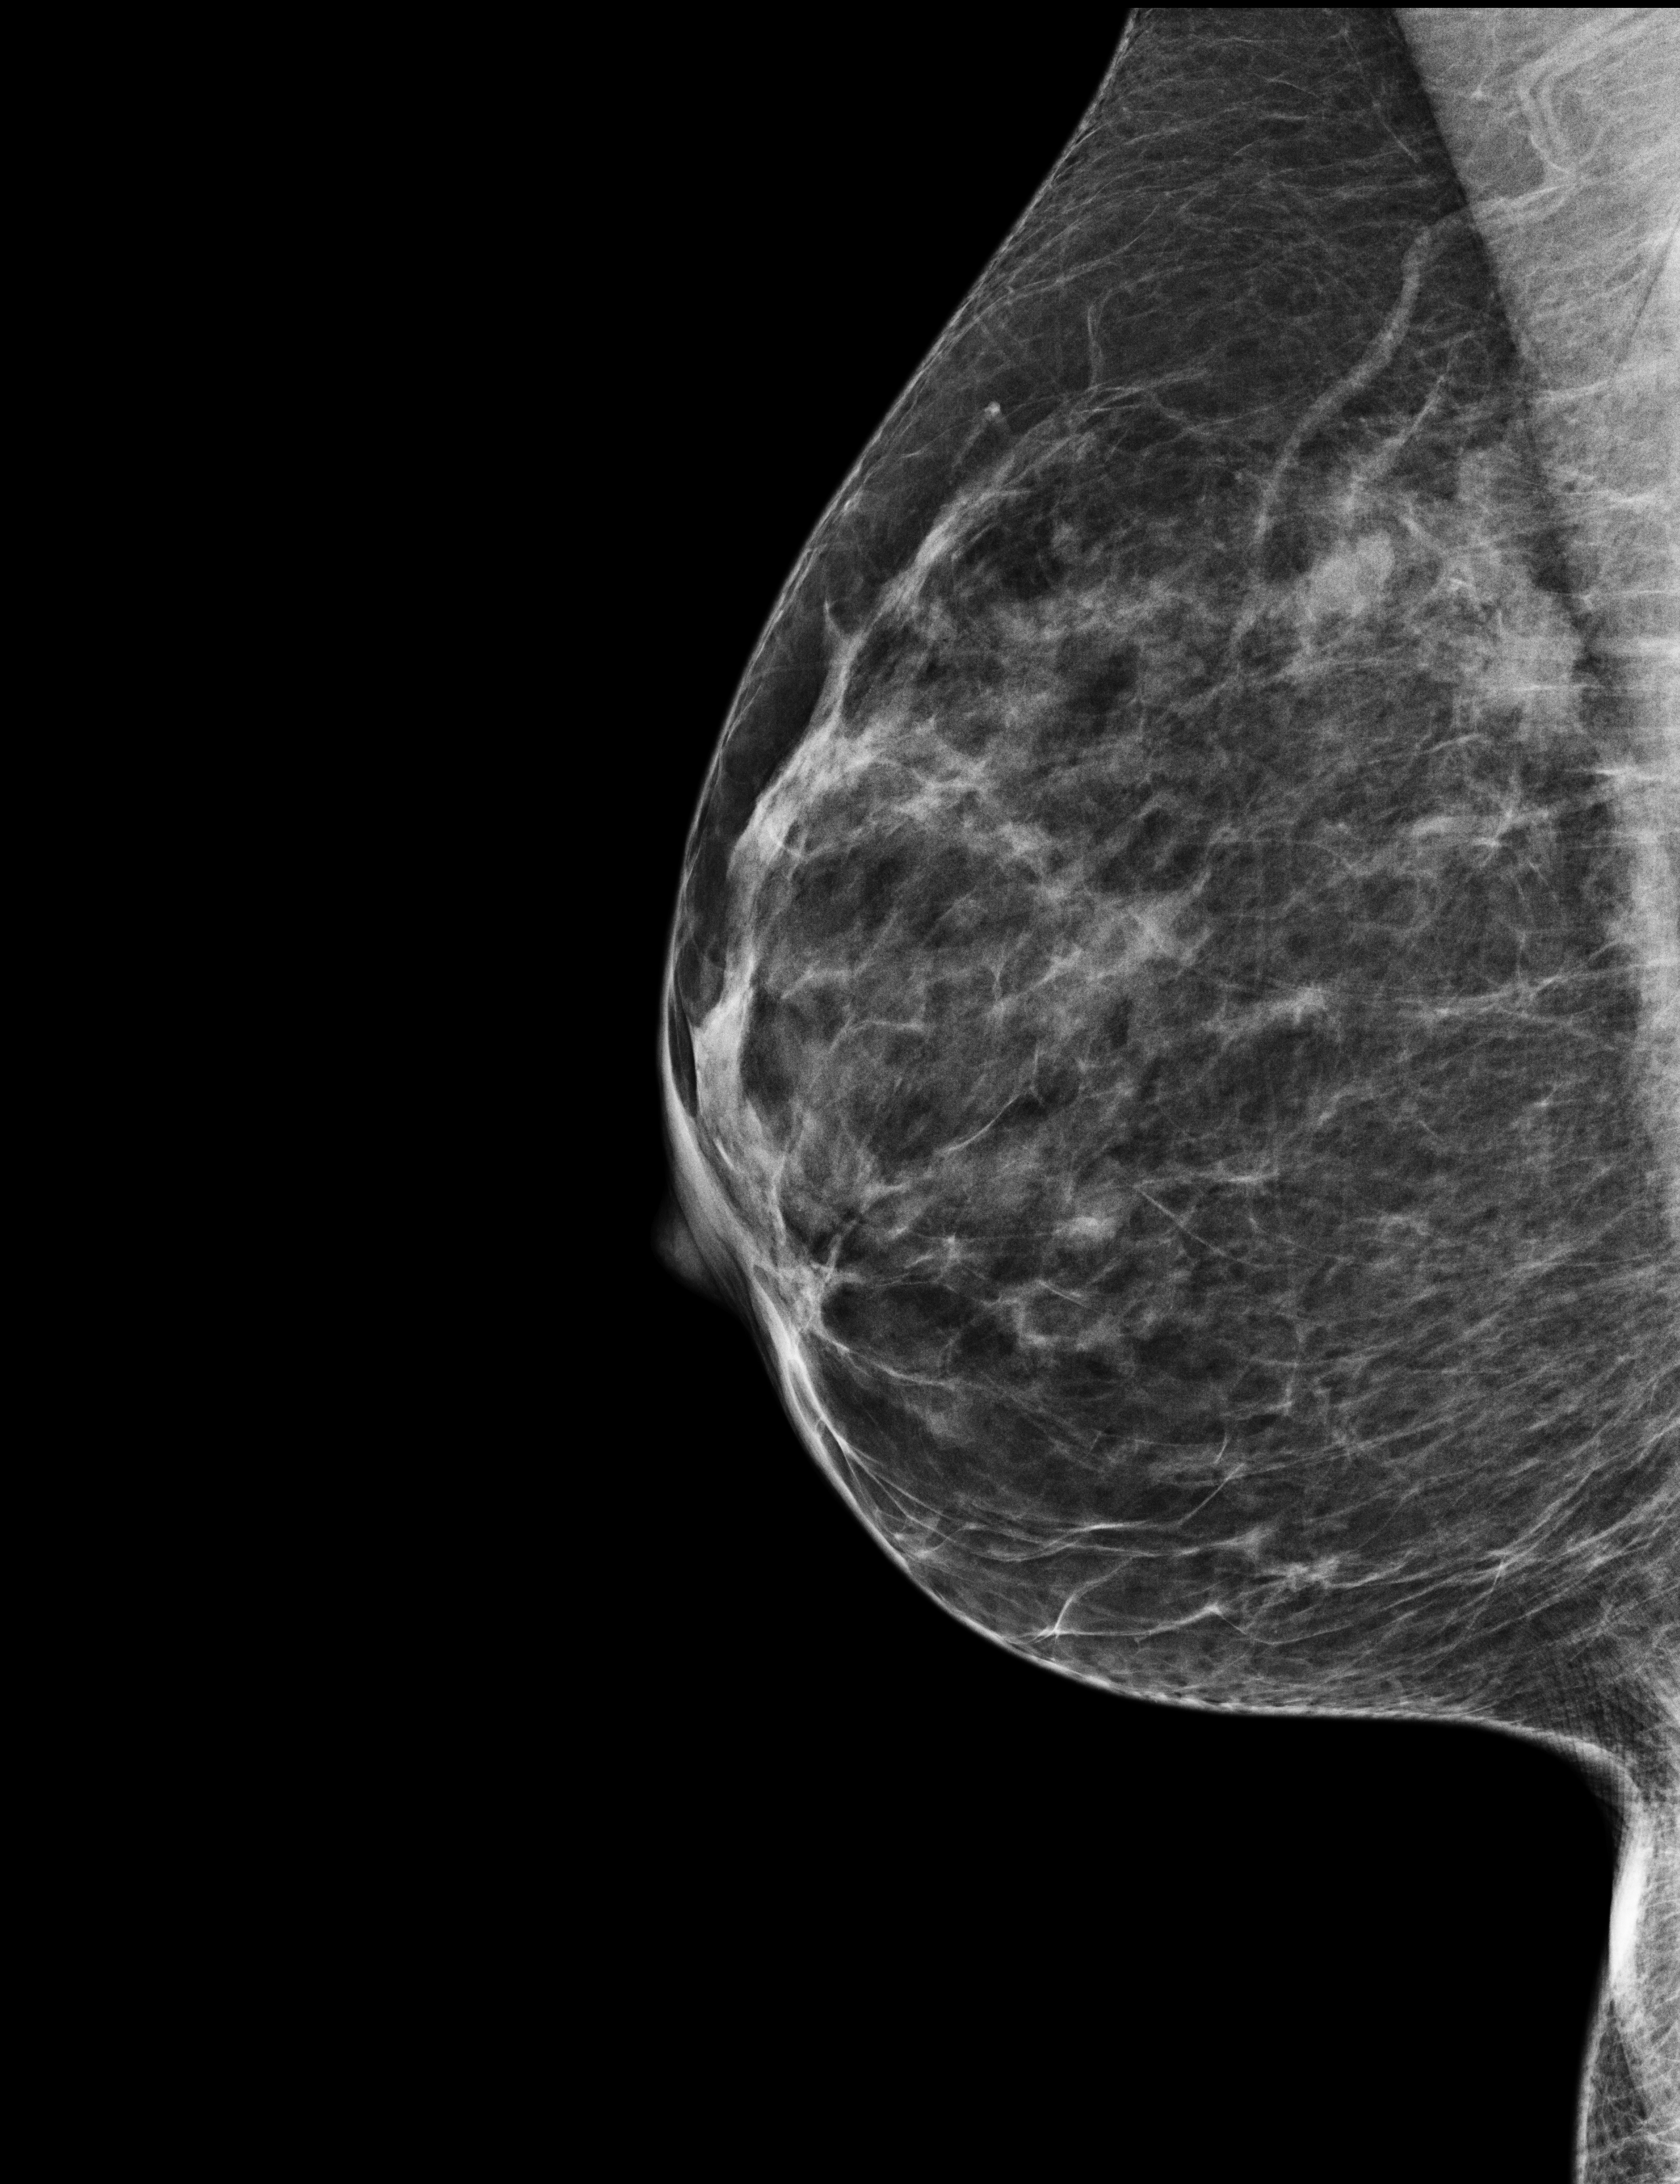
Diagnostic examination (additional views), system: Selenia Dimensions.
Image type: full-field digital mammogram. Breast: right. Projection: ML view.